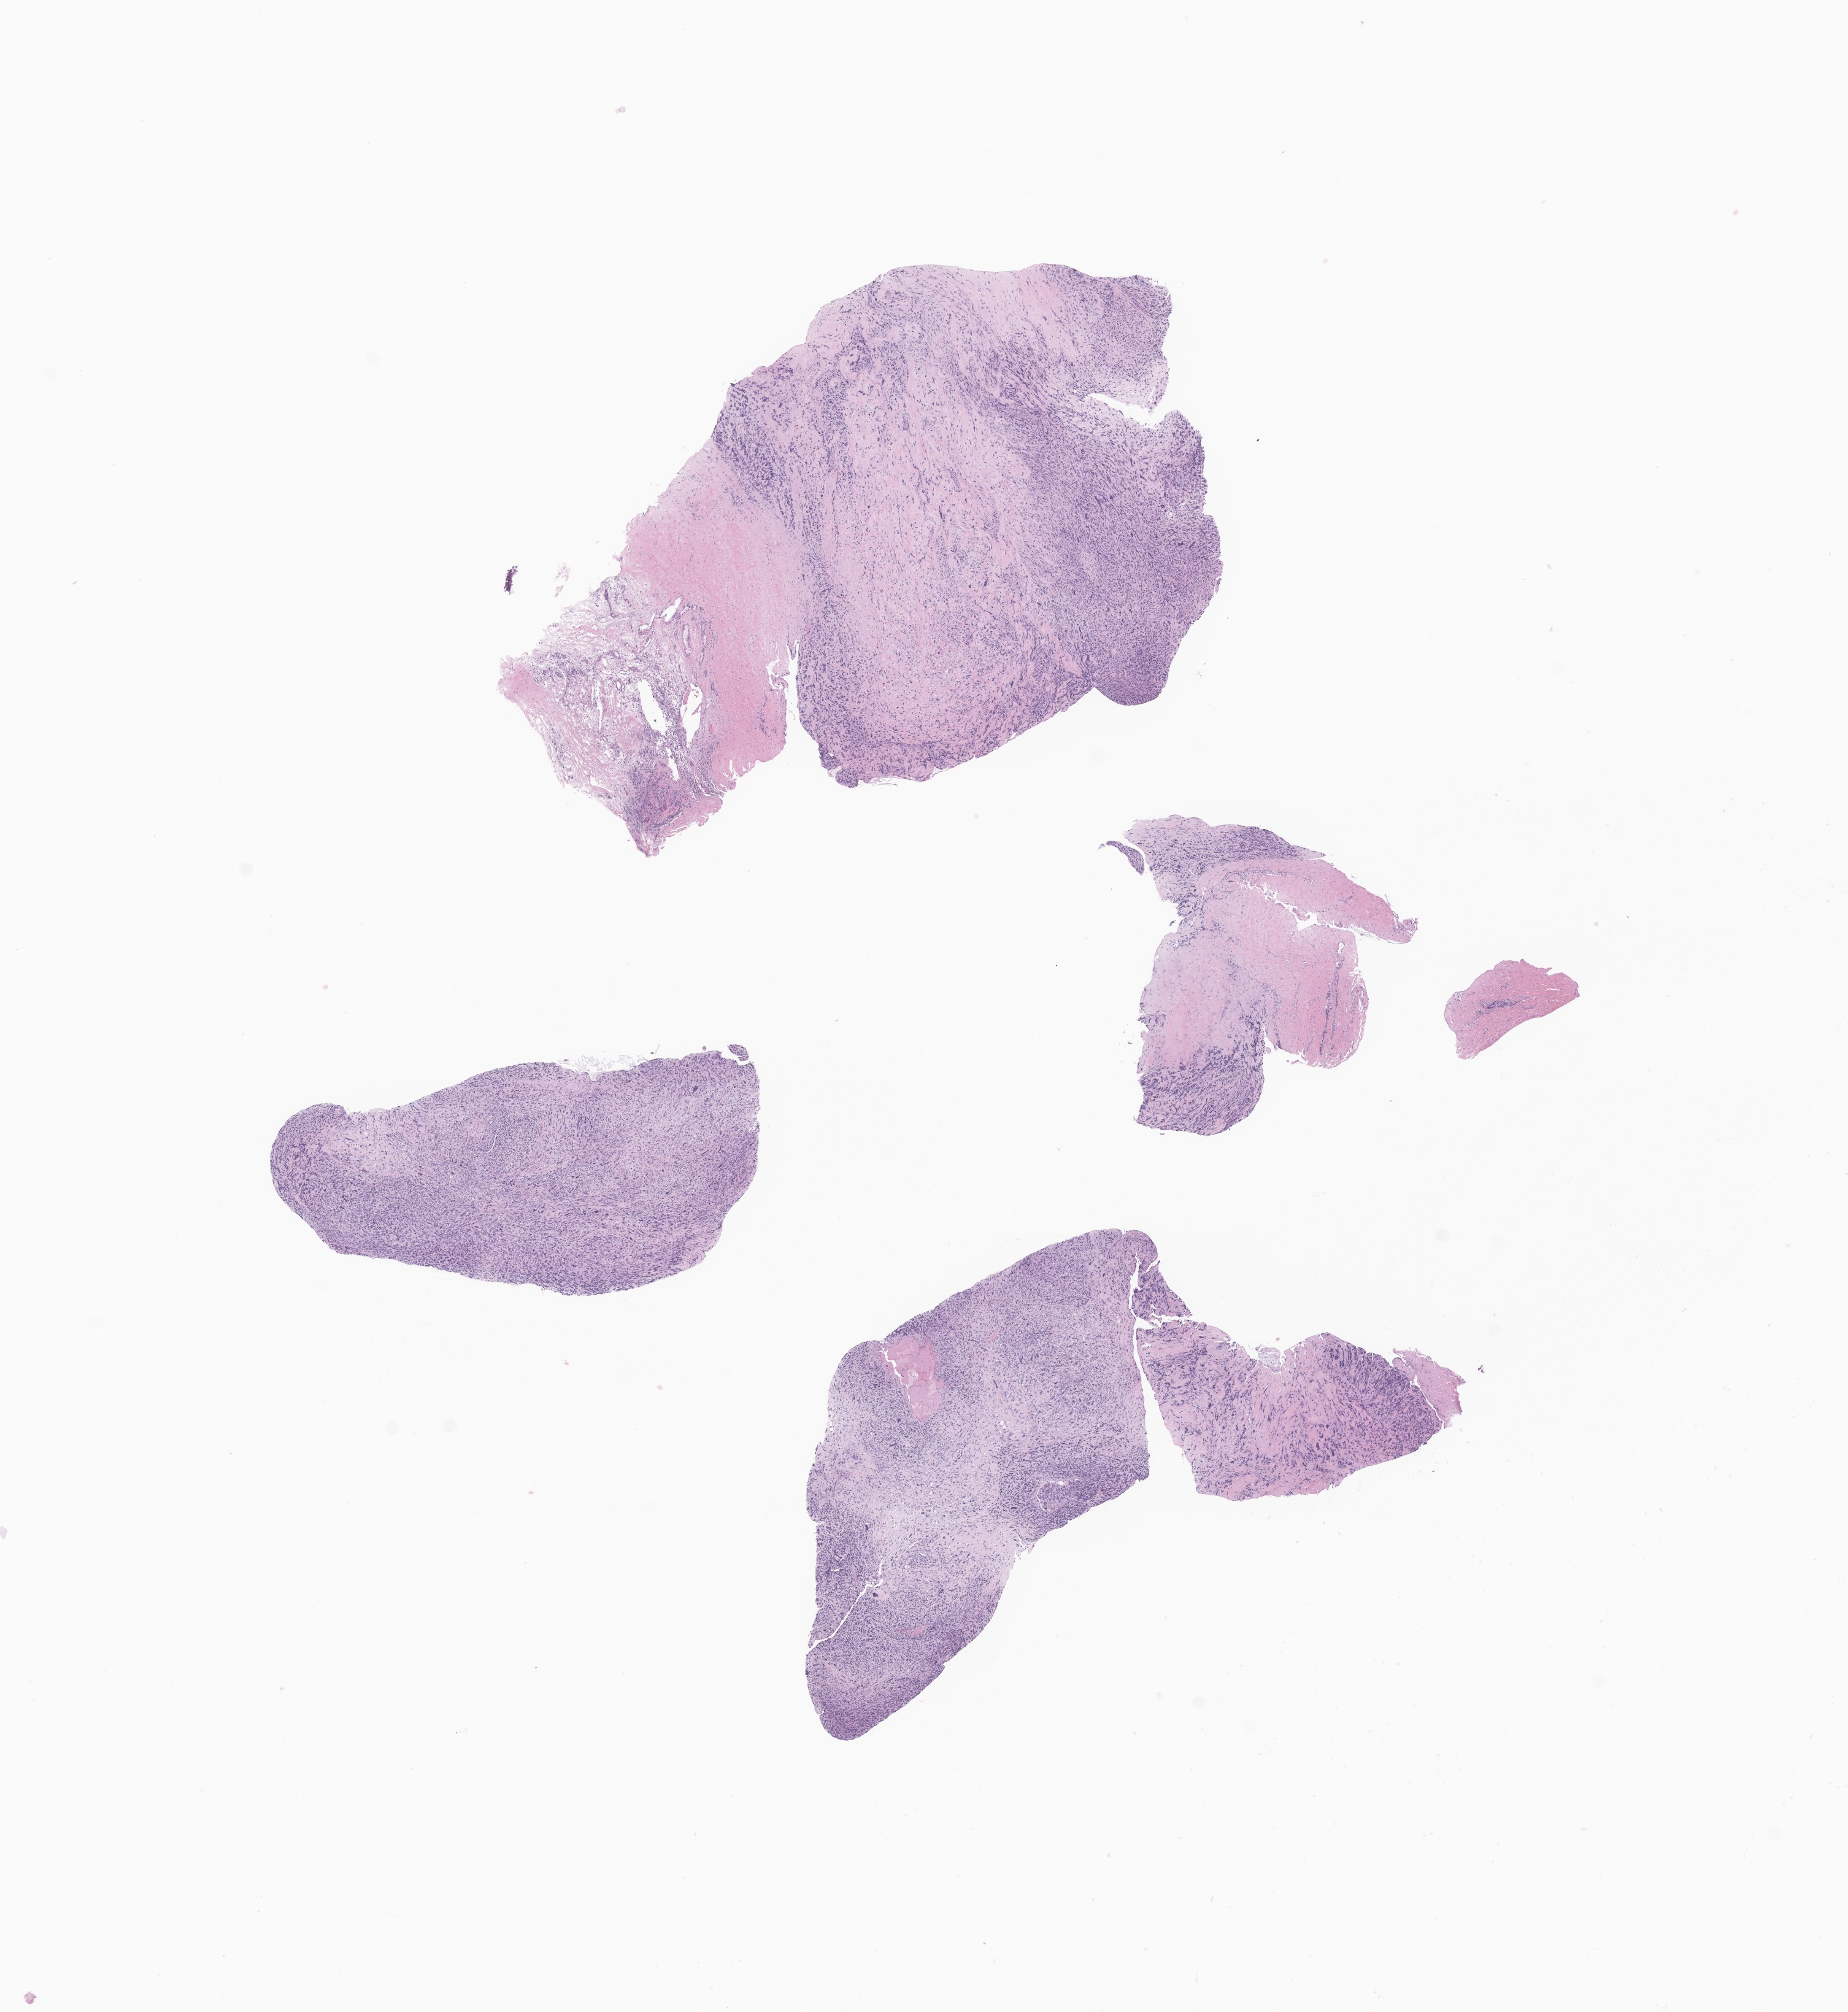
H&E whole-slide image of tumor tissue from the lateral wall of nasopharynx — a low-resolution overview of the entire scanned area, about 12.7 x 13.8 mm; formalin-fixed paraffin-embedded section. Patient male; age 127 months (10 years 7 months).
- diagnosis: Embryonal rhabdomyosarcoma, NOS